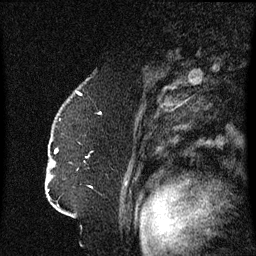
Breast MRI (dynamic contrast-enhanced), one sagittal slice. Position 46 of 60 along the scan axis. Dynamic contrast-enhanced series, image 2 of 3 at this slice position (ordered by acquisition). 1.5 T. TE 4.2 ms, TR 8.4 ms. 256 × 256 image matrix, field of view 200 × 200 mm. Patient: female, 52 years. From the clinical record (not read from this slice): setting: breast cancer imaged before/during neoadjuvant chemotherapy; receptor status: HR-positive, HER2-negative.
Structures marked on this image (semi-automatically segmented with operator editing):
- analysis volume of interest (the breast-tissue region the enhancement analysis was run in; not a lesion): box from (x=49, y=124) to (x=125, y=197) px
- tumour enhancement mask (voxels above the 70 % enhancement threshold inside the analysis volume of interest): (x=55, y=148)–(x=58, y=153)